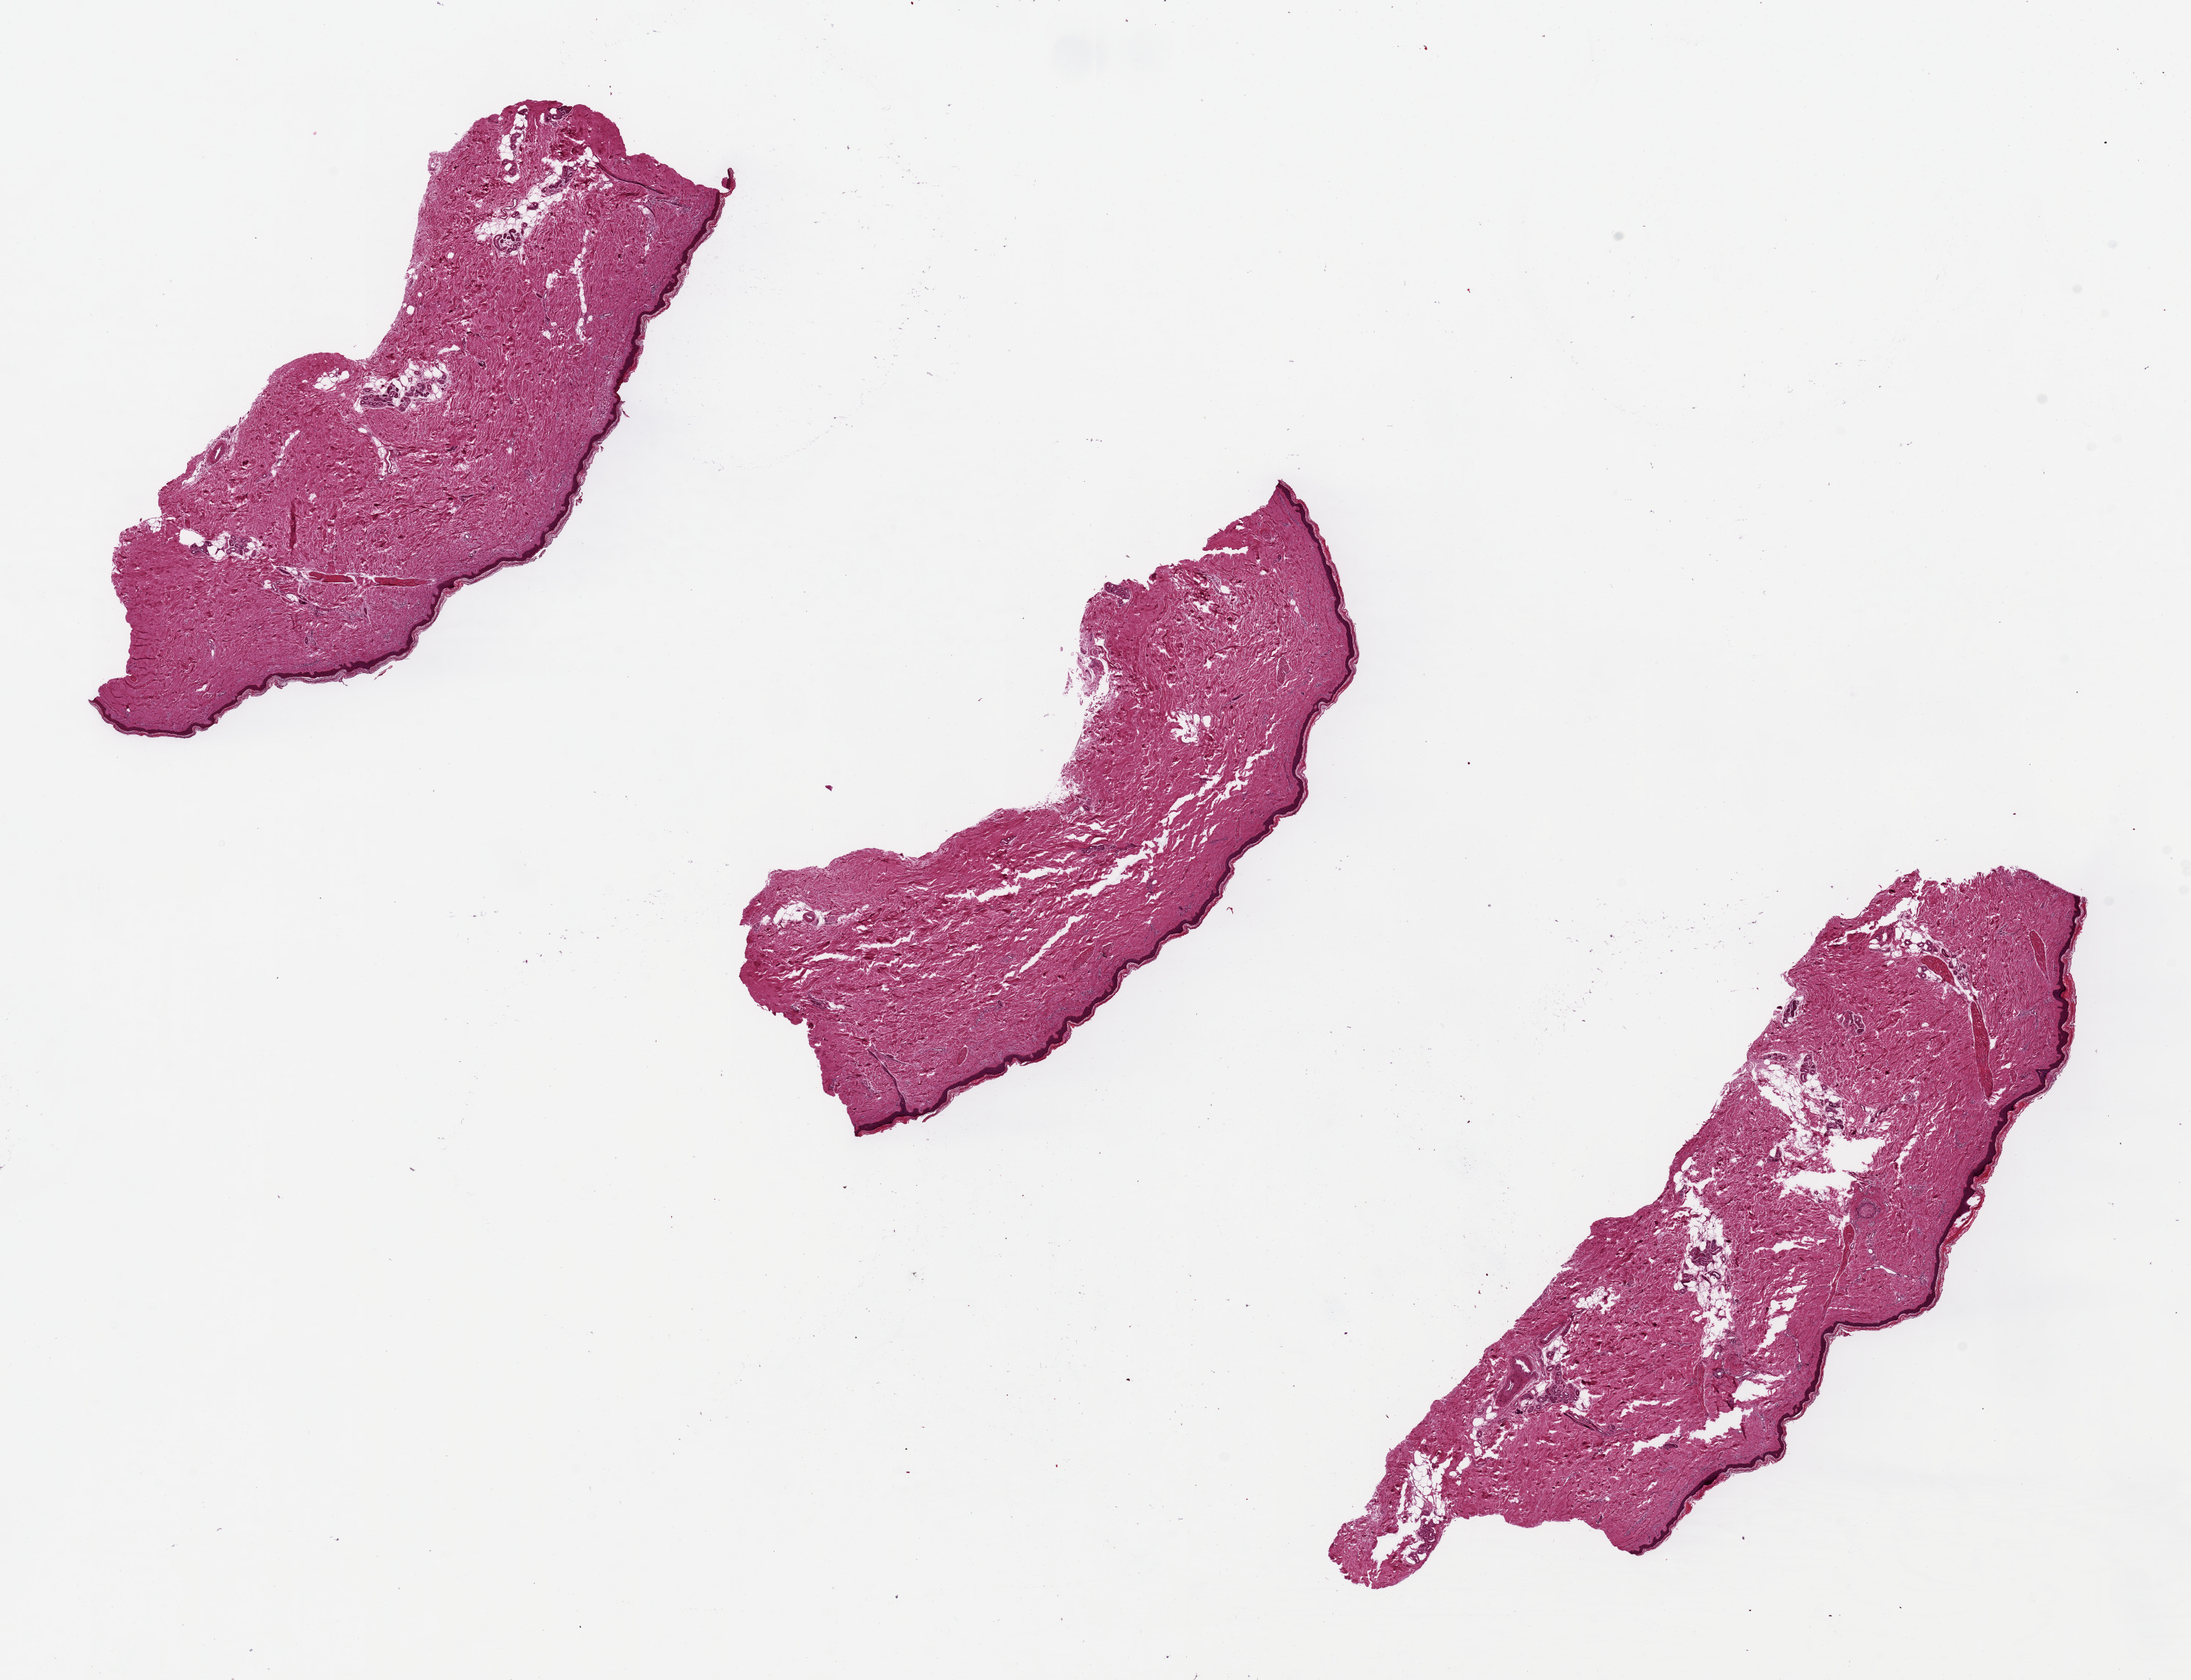
Digitized haematoxylin and eosin-stained section, brightfield — whole scanned area (about 23.6 x 18.1 mm, from a 20x scan) shown as a low-resolution overview; PAXgene-fixed paraffin-embedded (PFPE) section; section of skin of lower leg (target tissue); tissue donor sample. Donor sex: male.
Reviewer comment on this tissue sample: Epidermis is 3% of aliquot thickness.